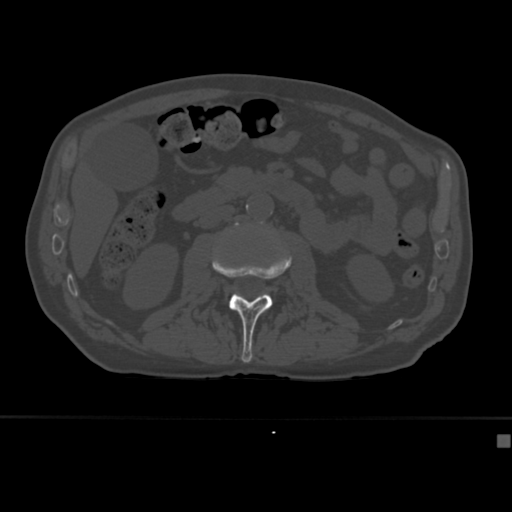
CT including the spine, one axial slice; position 143 of 430 along the scan axis; reconstruction kernel Br40s; 120 kVp; bone window (W 1800 / L 400 HU); 1.5 mm slice thickness; 512 × 512 image matrix, field of view 337 × 337 mm. Patient: male, 64 years. From the clinical record (not read from this slice): primary cancer: uterus; vertebrae with lytic lesions (as recorded): T1, T4, T5, T7, L5.
Structures marked on this image (semi-automatically segmented with operator editing):
- L2 vertebra: bounding box <212,236,292,363> (left, top, right, bottom; pixels)